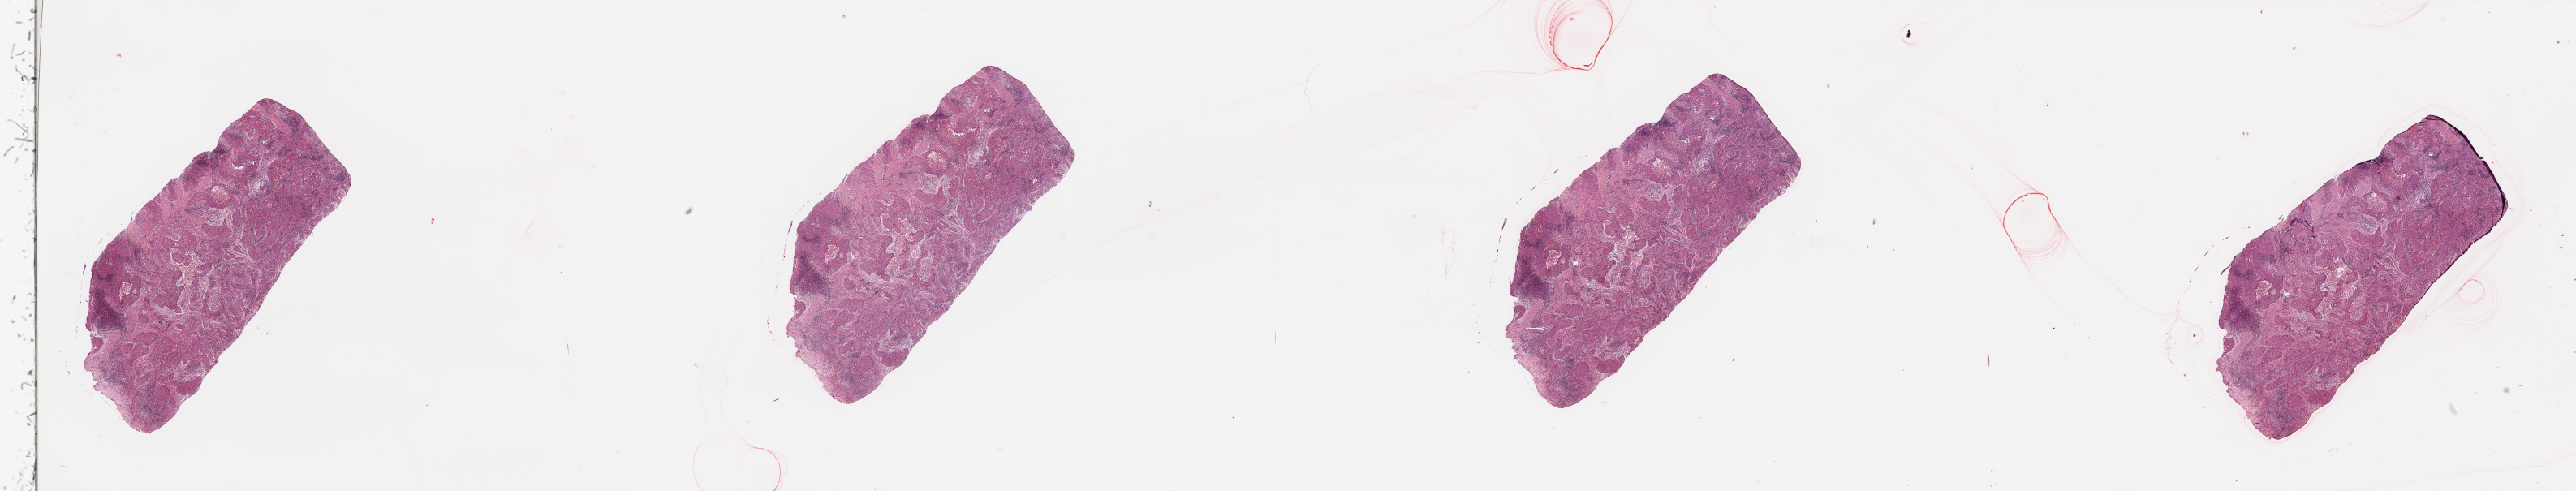
H&E-stained whole-slide image — whole scanned area (about 50.2 x 9.6 mm, from a 20x scan) shown as a low-resolution overview. Tumour tissue sample, sampled site: larynx. Male, 68 y/o. Histologic grade: G3 (poorly differentiated). Composition of this section per pathologist review: tumour nuclei 85%, necrosis 3%.
• primary tumour site (as recorded): larynx
• AJCC pathologic stage: I
• histologic diagnosis: Squamous cell carcinoma, NOS (larynx, NOS)